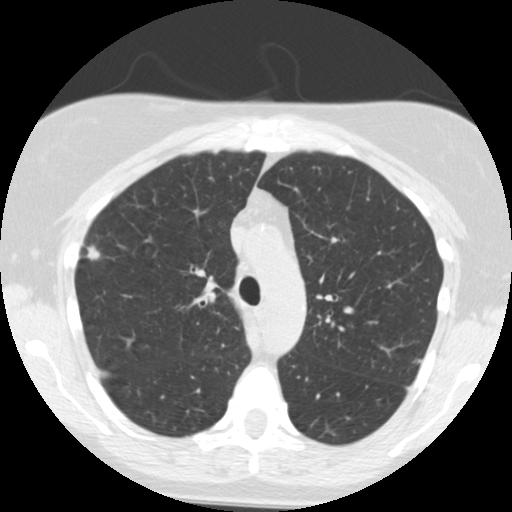
Low-dose screening chest CT, axial slice. Second screening round (one year after baseline). Lung window (W 1500 / L -600 HU). Standard (soft-tissue) reconstruction kernel (STANDARD). 512 × 512 image matrix, field of view 312 × 312 mm. Female, age 55 years at enrolment. Current smoker at enrolment.
Lesion marked by an expert reader, bounding box (x1, y1, x2, y2) in pixels: (69, 237, 114, 277). Screening reader's record for this exam: no non-calcified nodule ≥4 mm recorded. Official screen result: negative screen, minor abnormalities not suspicious for lung cancer. Later outcome: lung cancer diagnosed 621 days after this screen (after the third annual screen) — bronchiolo-alveolar adenocarcinoma, NOS, right upper lobe, moderately differentiated (G2), stage IIA (AJCC 6th edition), 13 mm at pathology.